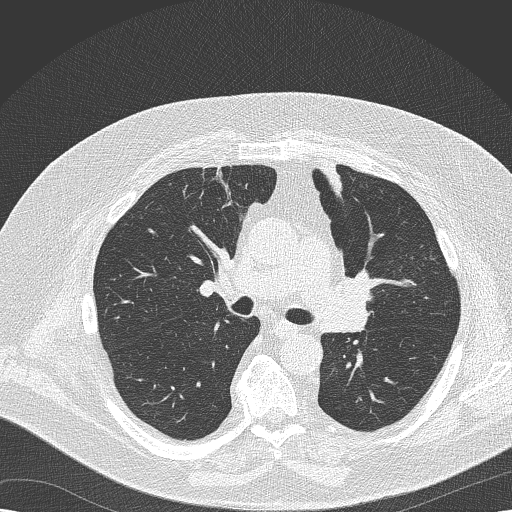
Chest CT (low-dose screening protocol), one axial image. Second annual screen. Lung window (W 1500 / L -600 HU). Slice 71 of 173 in the series. Male, age 68 years at enrolment. Former smoker at enrolment.
- Expert-annotated lung lesion, bounding box (x1, y1, x2, y2) in pixels: (321, 263, 384, 325).
- Screening reader's record for this exam (one nodule recorded; not confirmed to be the boxed lesion): non-calcified nodule or mass ≥4 mm, left lower lobe, 8 × 6 mm, soft tissue attenuation, pre-existing on the prior screen: yes; interval growth: no.
- Official screen result: positive, no significant change: stable abnormalities potentially related to lung cancer, unchanged since the prior screening exam.
- Later outcome: lung cancer diagnosed 256 days after this screen — squamous cell carcinoma, NOS, left upper lobe, poorly differentiated (G3), stage IIB (AJCC 6th edition), 35 mm at pathology.